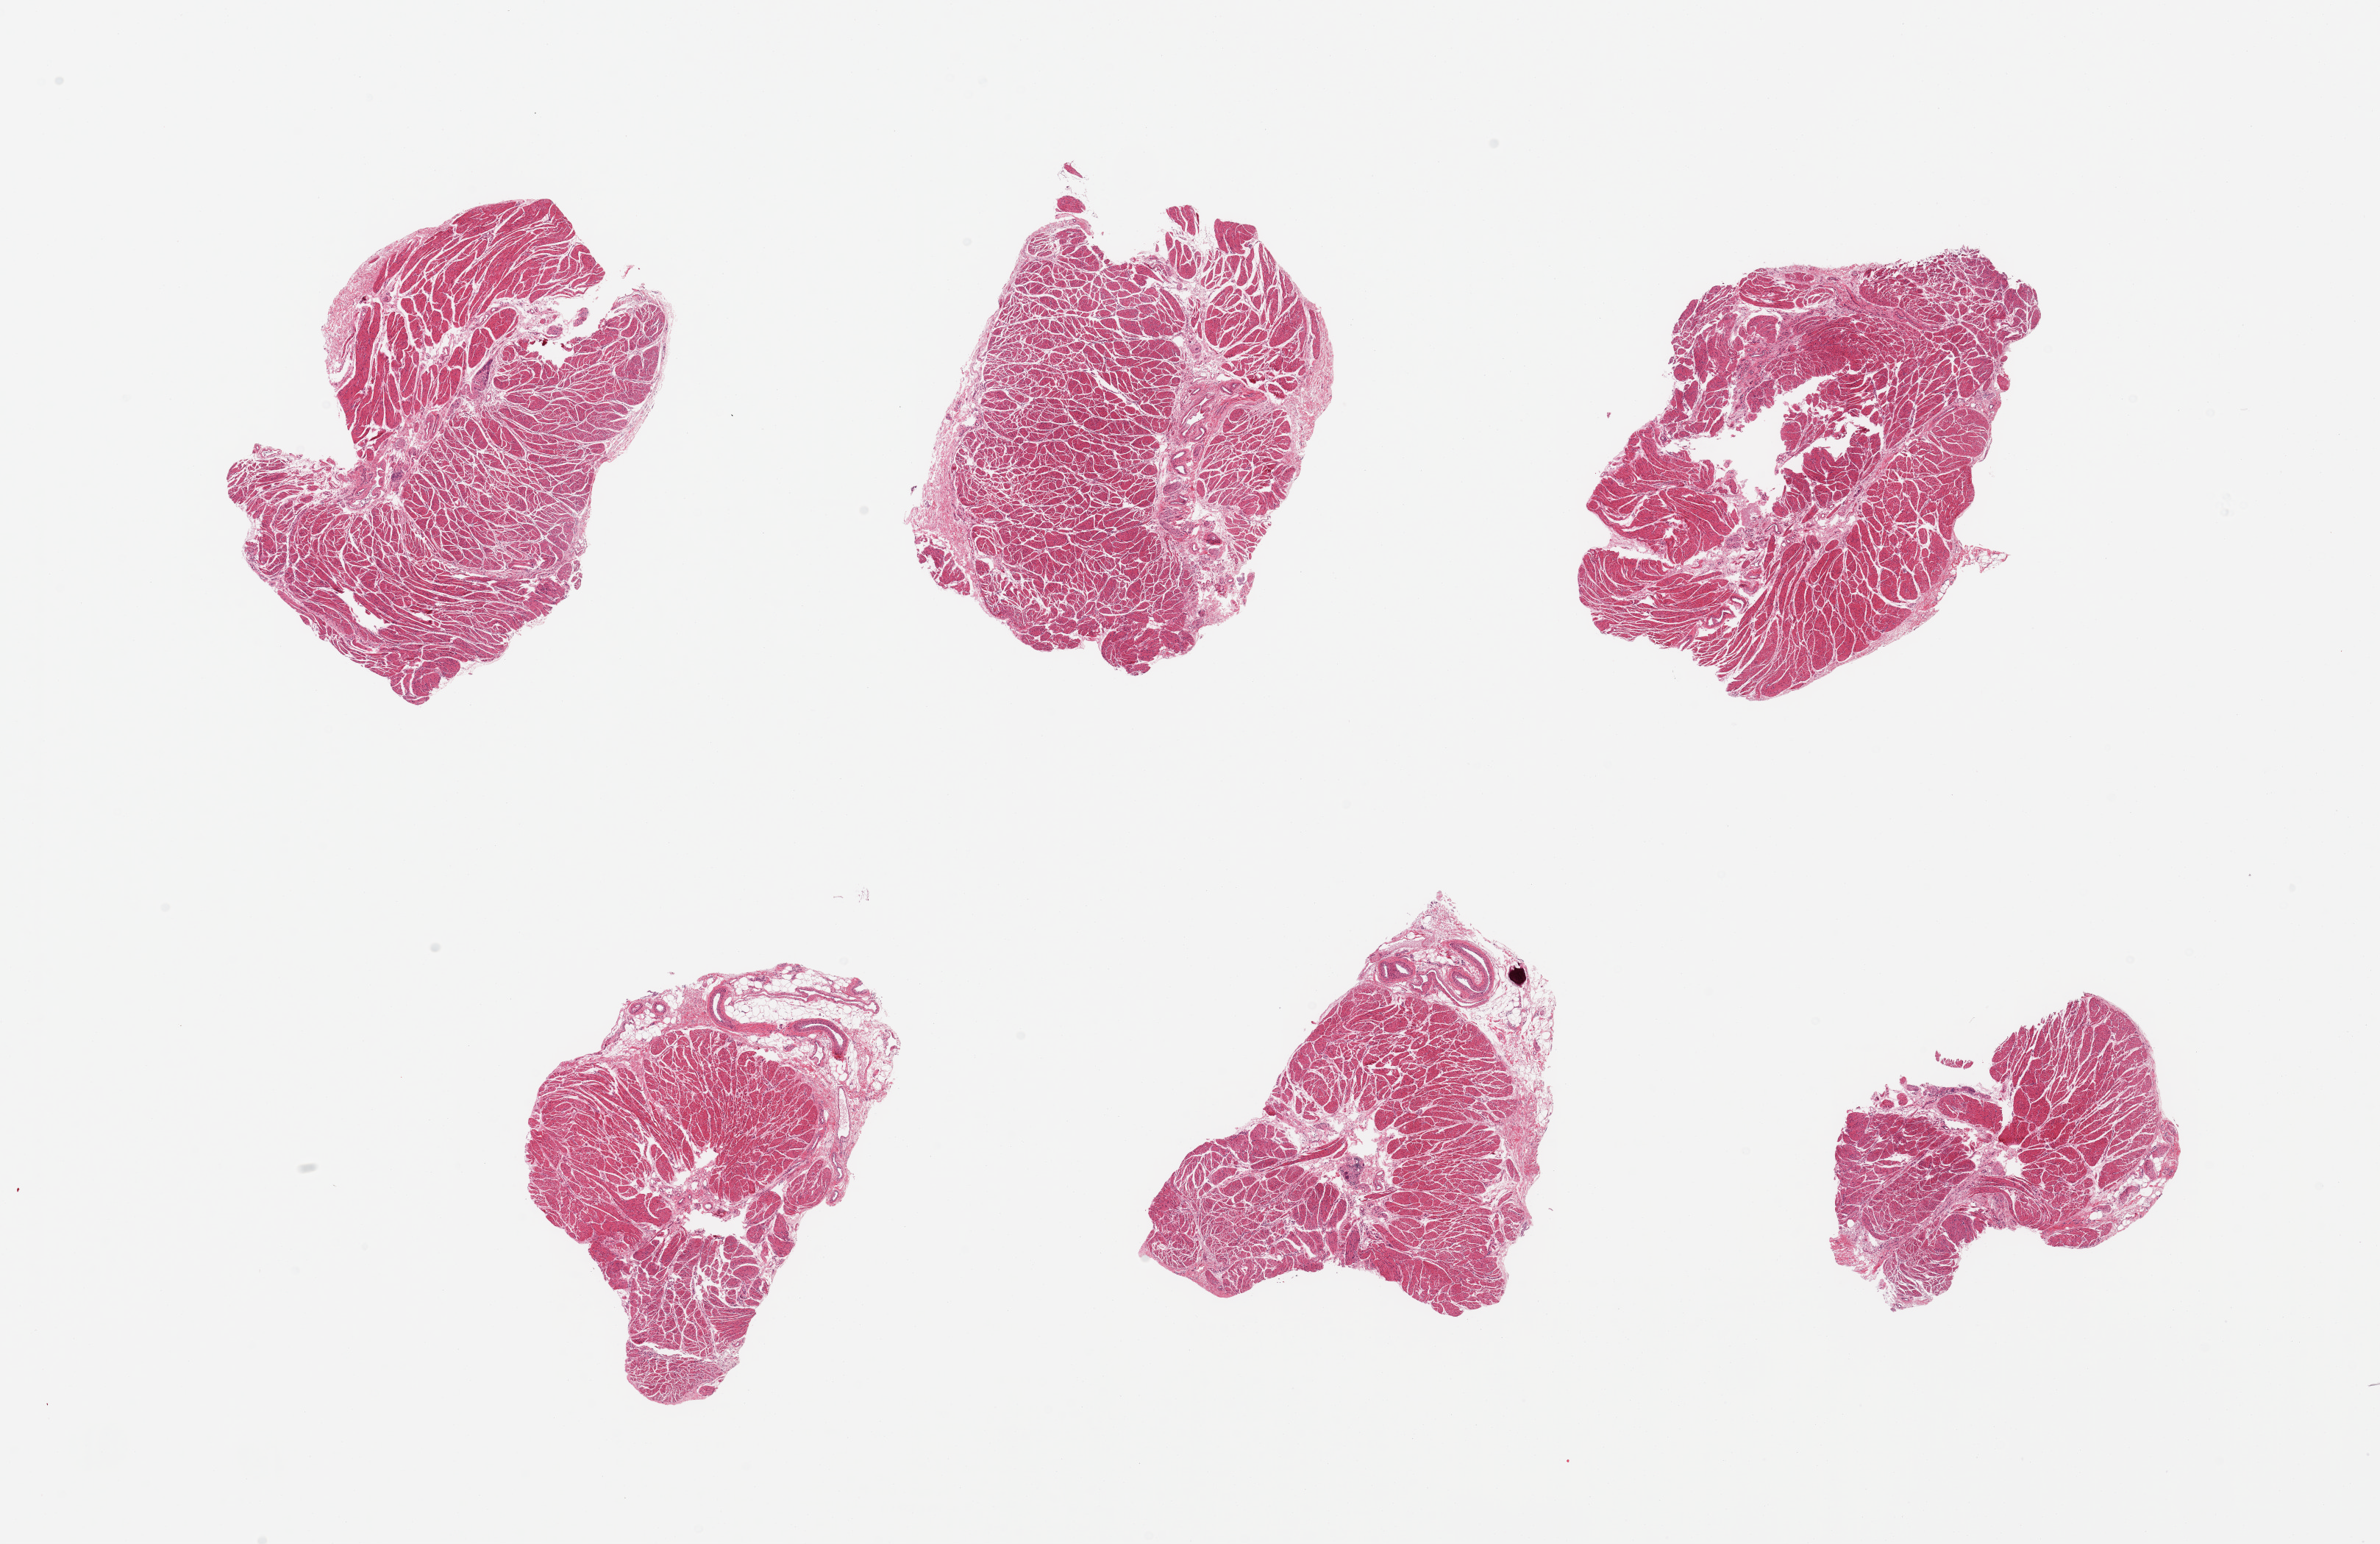
Digitized H&E-stained section, brightfield, low-resolution overview of the scanned area, about 25.6 x 16.6 mm (acquisition: 20x scan), PAXgene-fixed, paraffin-embedded tissue, sampled site (target tissue): gastroesophageal junction, donor tissue sample. Male donor.
Pathologist's review note for this sample: 6 pieces; target muscularis, small attachment of fat/nerve.